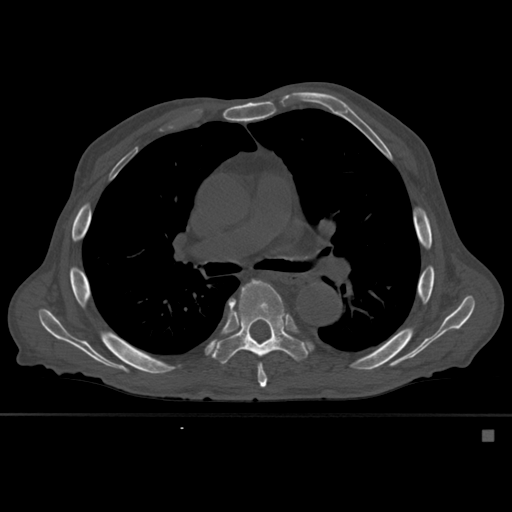
CT including the spine, one axial slice. Bone window (W 1800 / L 400 HU). 1.5 mm slice thickness. 512 × 512 image matrix, field of view 373 × 373 mm. Male patient, age 78 years. Case-level facts recorded for this patient, not image findings: primary cancer: prostate.
Annotated regions visible in this slice (semi-automatically segmented with operator editing):
- T6 vertebra: box from (x=232, y=280) to (x=276, y=388) px
- T7 vertebra: (x=210, y=280)–(x=310, y=364)